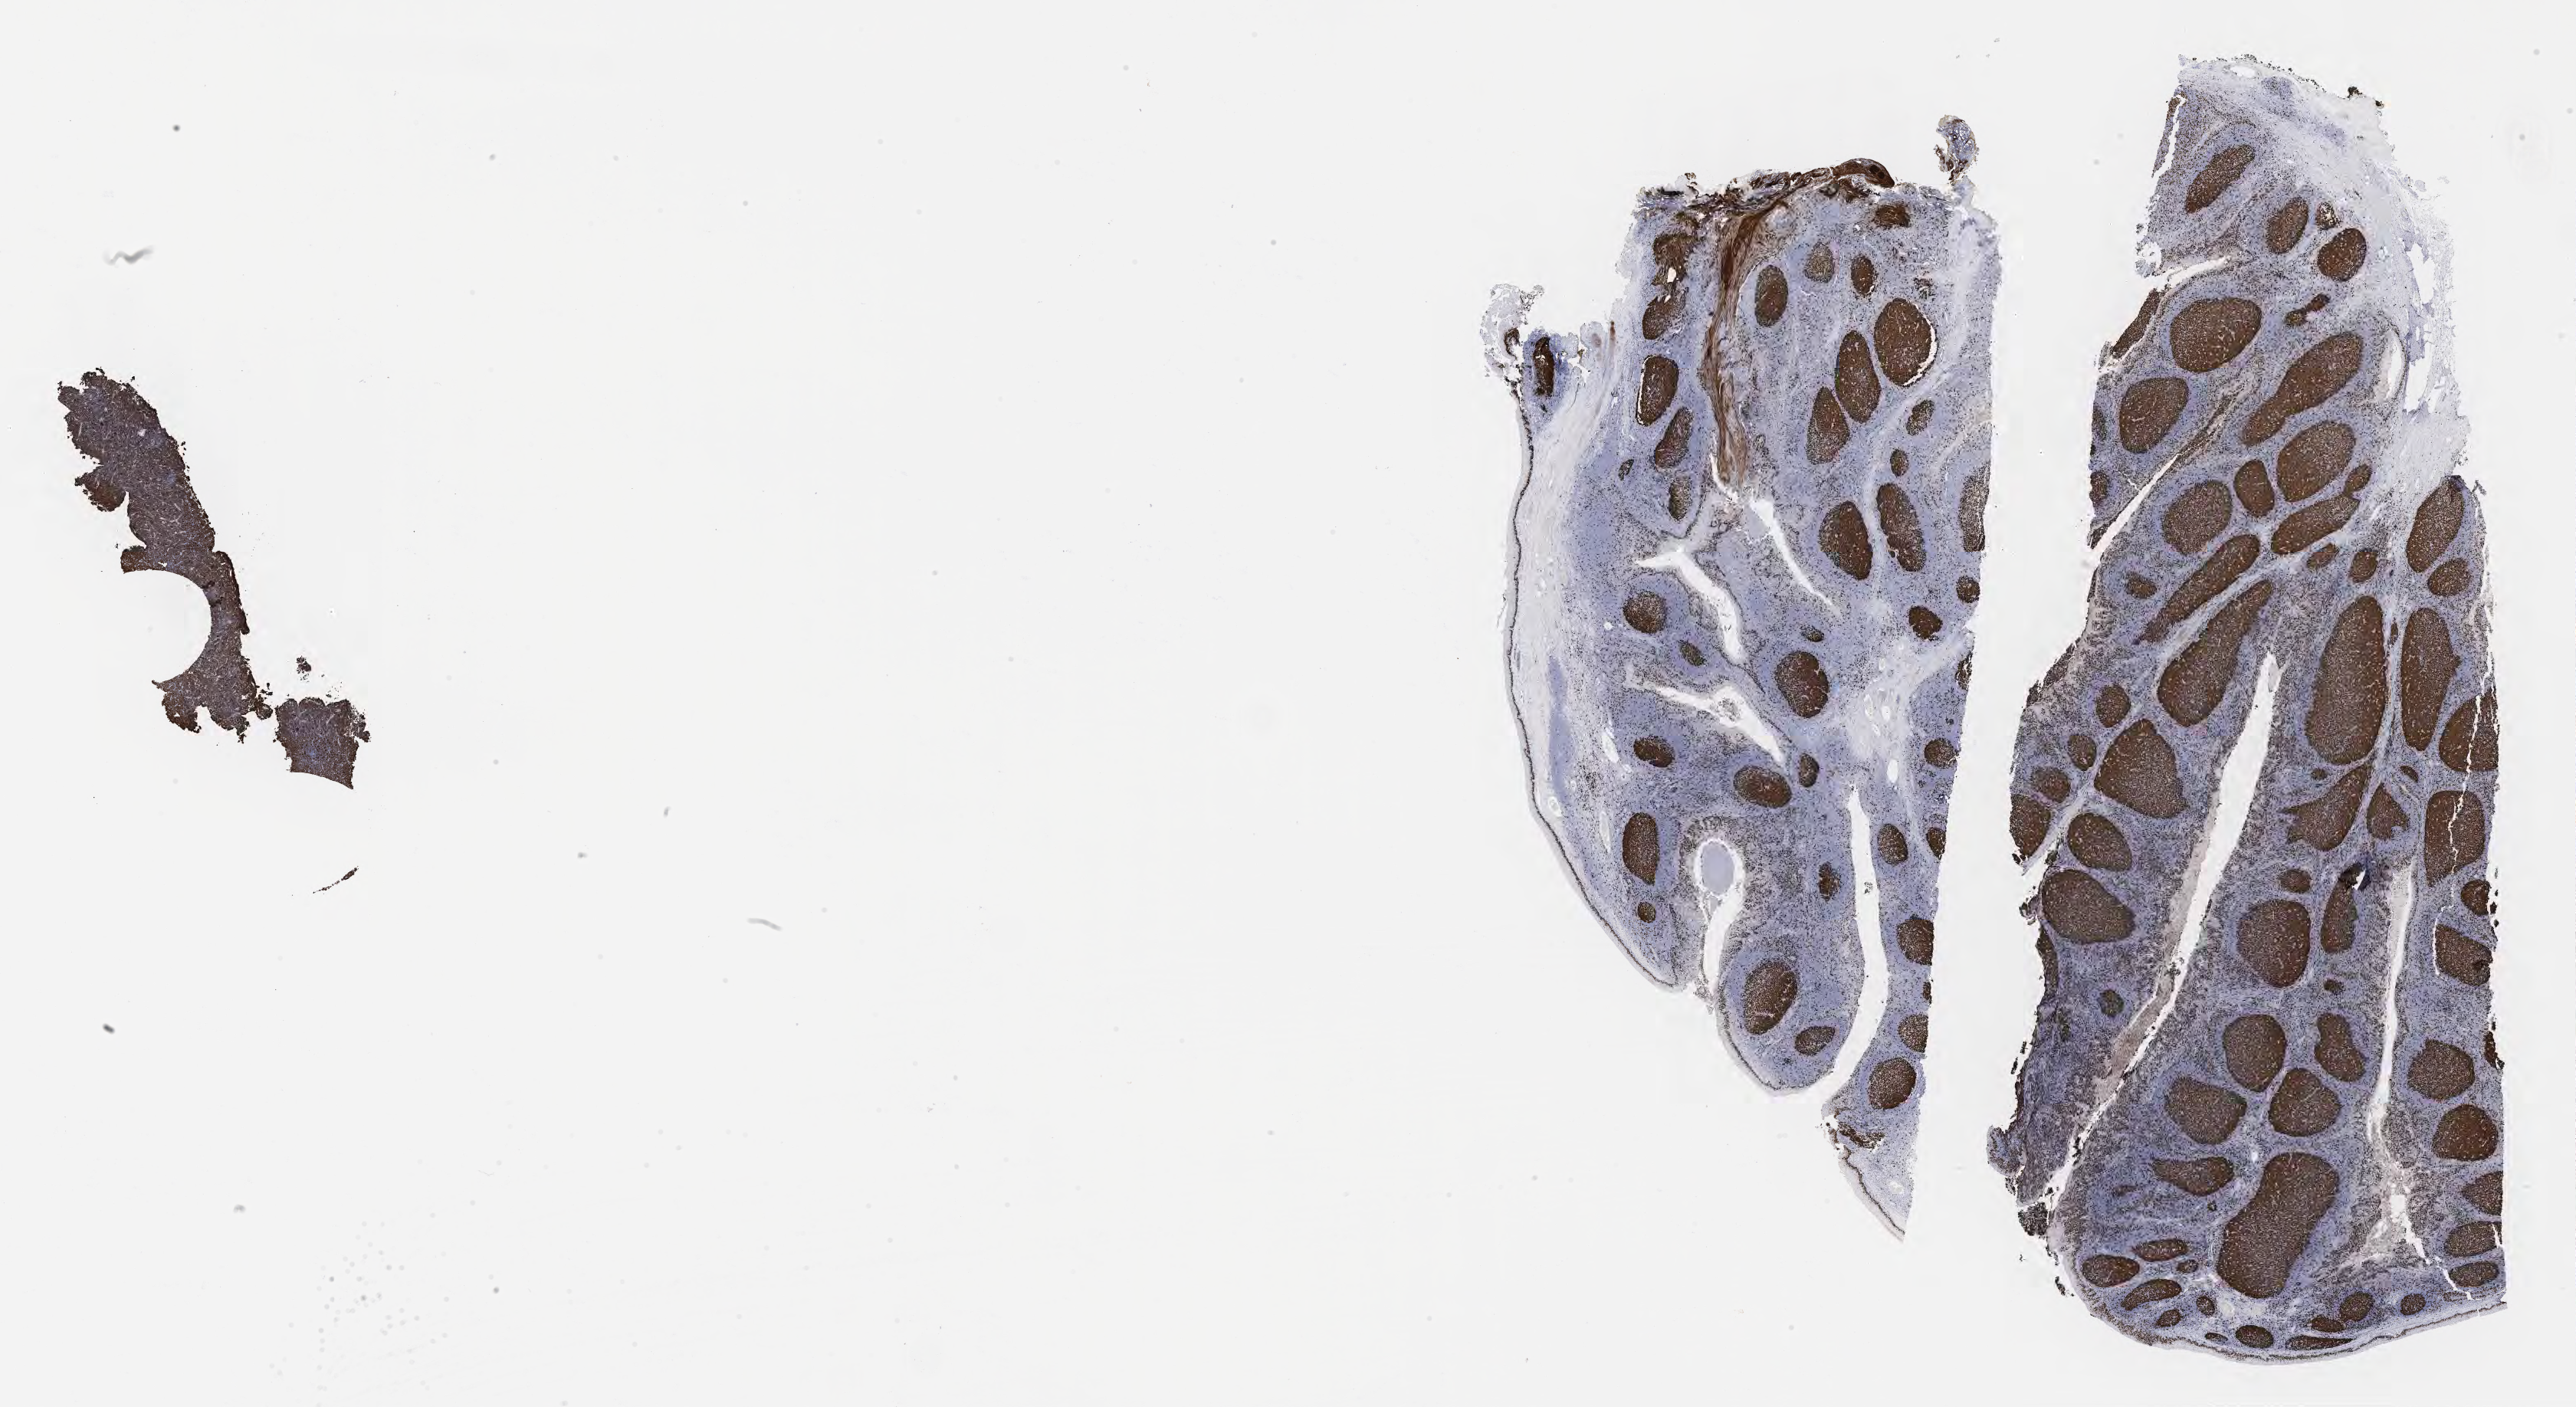
Whole-slide image, immunohistochemical stain for Ki-67, low-resolution overview of the scanned area, about 27.2 x 14.8 mm, tumor tissue. Patient: male, age at initial diagnosis 5 years.
- diagnosis: Burkitt lymphoma, NOS